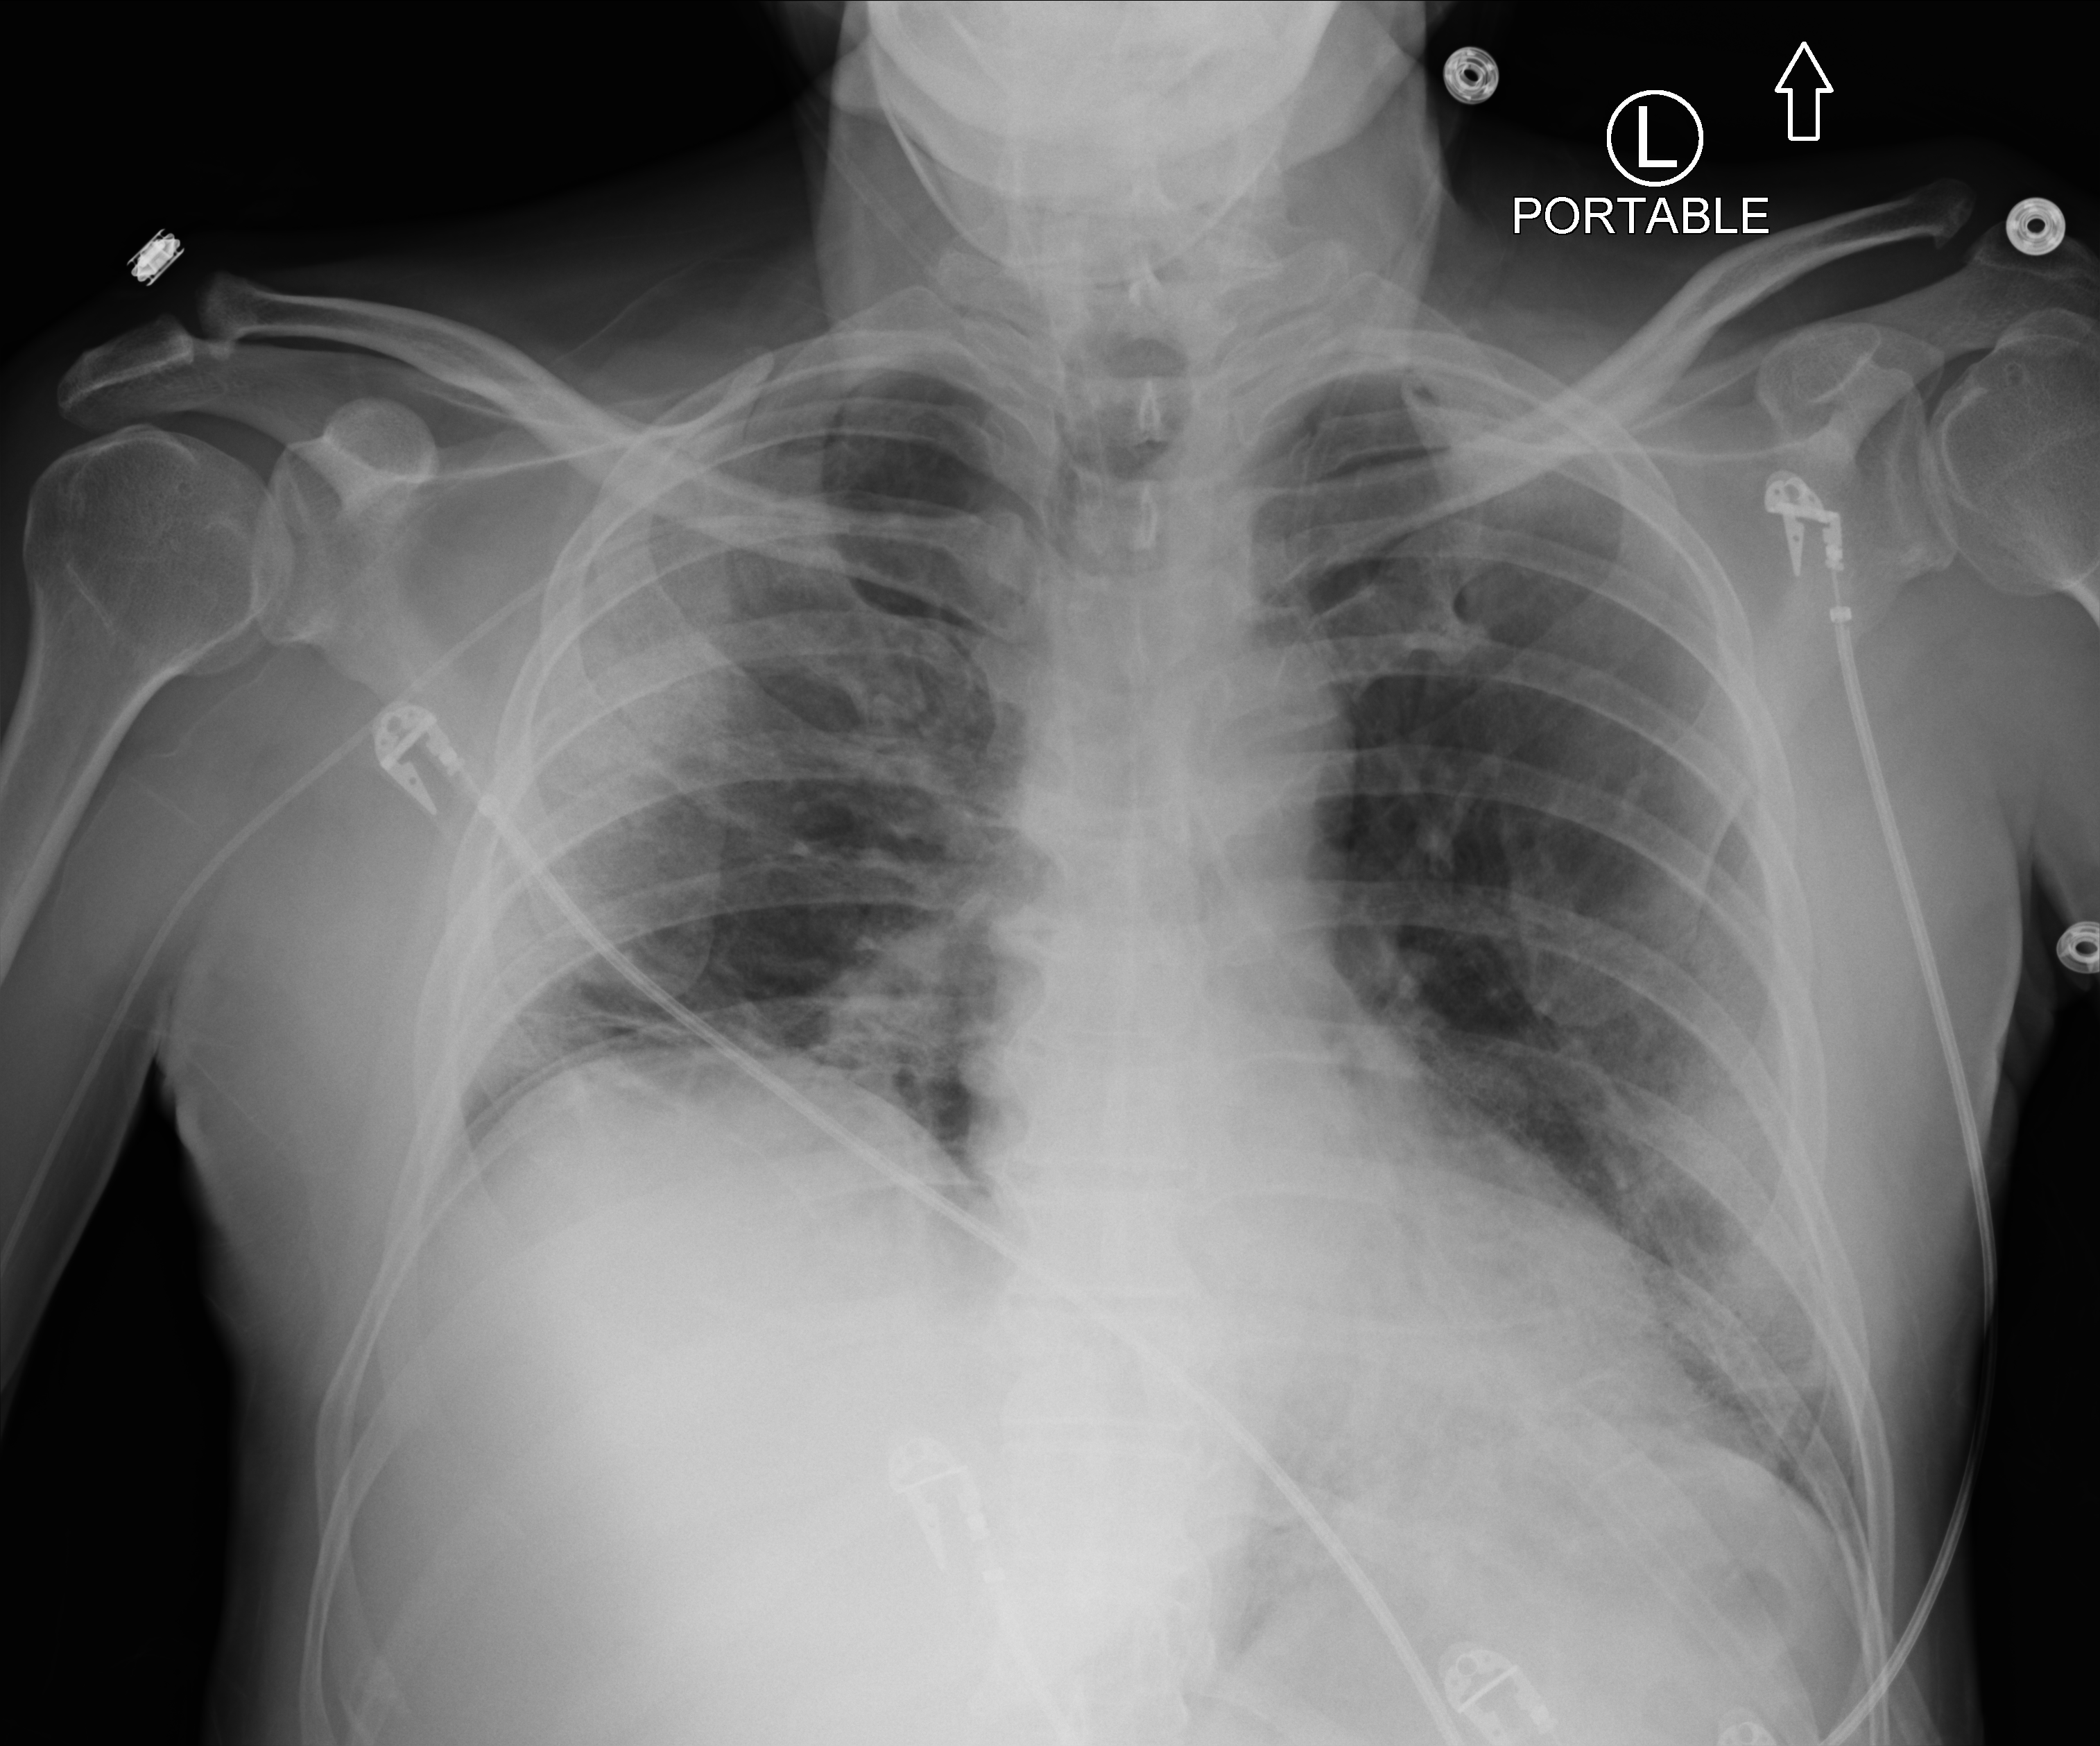
Portable chest radiograph. Male patient hospitalised with COVID-19, age 60–74 years.
From the hospital-stay record, not from the radiograph (when in the stay this image was taken is not recorded): hypertension (admission record): yes; diabetes (admission record): no.